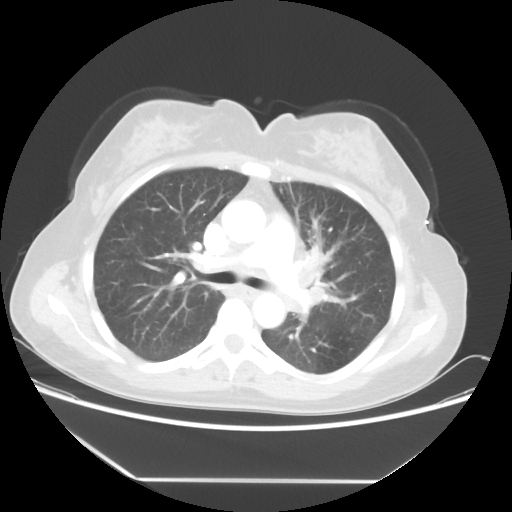
Chest CT, one axial slice. Slice 33 of 52 in the series (ordered by position). 100 kVp. Lung window (W 1500 / L -600 HU). 5 mm slice thickness. 512 × 512 image matrix, field of view 390 × 390 mm. Female patient, age 50 years. Case-level facts recorded for this patient, not image findings: clinical TNM (as recorded): T2 N3 M0.
Annotated regions visible in this slice (bounding box drawn by a radiologist):
- lung tumour (recorded histology: adenocarcinoma): bounding box <289,215,342,326> (left, top, right, bottom; pixels)